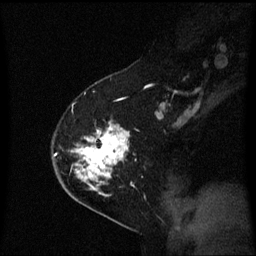
Breast MRI (dynamic contrast-enhanced), one sagittal slice. Dynamic contrast-enhanced series, image 2 of 3 at this slice position (ordered by acquisition). 1.5 T. TE 4.2 ms, TR 8.4 ms. 2 mm slice thickness. 256 × 256 image matrix, field of view 210 × 210 mm. Patient: female, 54 years. From the clinical record (not read from this slice): setting: breast cancer imaged before/during neoadjuvant chemotherapy; receptor status: HER2-positive.
Annotated regions visible in this slice (semi-automatic segmentation, software-assisted and operator-edited):
- analysis volume of interest (the breast-tissue region the enhancement analysis was run in; not a lesion): box from (x=59, y=120) to (x=137, y=199) px
- tumour enhancement mask (voxels above the 70 % enhancement threshold inside the analysis volume of interest): (x=78, y=126)–(x=130, y=191)